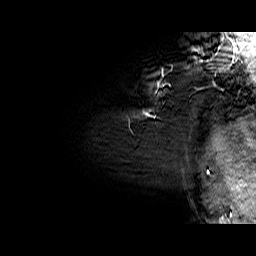
Breast MRI (dynamic contrast-enhanced), one sagittal slice. Position 58 of 60 along the scan axis. Dynamic contrast-enhanced series, time point 2 of 6 at this slice position (early post-contrast). 1.5 T. TE 6.4 ms, TR 32.9 ms. 256 × 256 image matrix, field of view 200 × 200 mm. Female patient. Case-level facts recorded for this patient, not image findings: setting: breast cancer imaged before/during neoadjuvant chemotherapy; receptor status: HER2-positive.
Annotated regions visible in this slice (semi-automatic segmentation, software-assisted and operator-edited):
- analysis volume of interest (the breast-tissue region the enhancement analysis was run in; not a lesion): bounding box [x1, y1, x2, y2] px = [132, 62, 210, 126]
- tumour enhancement mask (voxels above the 100 % enhancement threshold inside the analysis volume of interest): [157, 84, 159, 86]